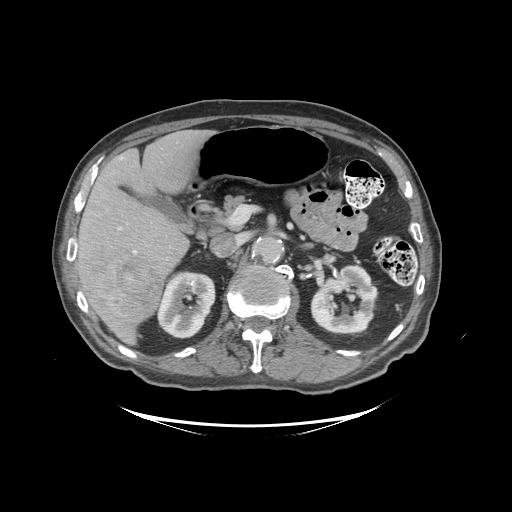
Contrast-enhanced abdominal CT (liver protocol), one axial slice. Reconstruction kernel STANDARD. 140 kVp. Soft-tissue window (W 400 / L 40 HU). 2.5 mm slice thickness. 512 × 512 image matrix, field of view 460 × 460 mm. From the clinical record (not read from this slice): diagnosis: hepatocellular carcinoma (patient treated with transarterial chemoembolisation; whether this scan precedes or follows treatment is not stated here); TNM stage (as recorded): Stage-I; Child-Pugh class: A; tumour nodularity: uninodular.
Structures marked on this image (semi-automatically segmented with operator editing):
- liver parenchyma outside the tumour (the mass and vessels are separate outlines, so this box may not span the whole liver): bounding box [x1, y1, x2, y2] px = [72, 130, 211, 342]
- mass: [89, 257, 162, 326]
- liver vessels: [73, 157, 137, 257]